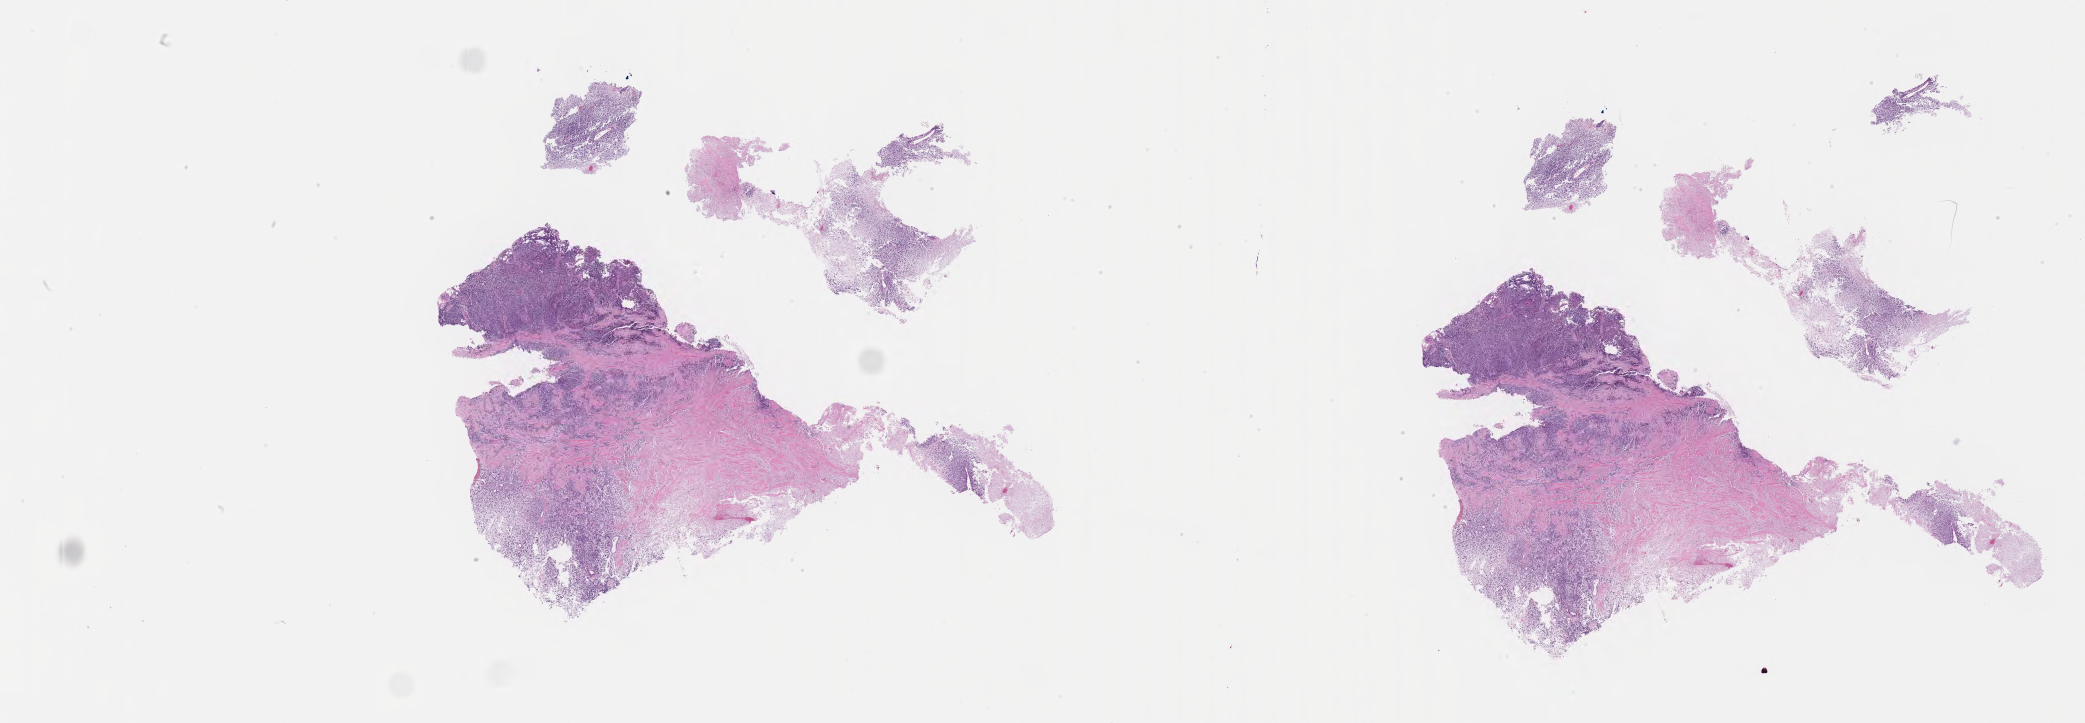
Whole-slide image, H&E stain of tumor tissue from the soft tissue of lower extremity, a low-resolution overview of the entire scanned area, about 33.7 x 11.7 mm, formalin-fixed paraffin-embedded section. Patient: male, age 145 months (12 years 1 month).
Diagnosis (ICD-O-3 morphology term): Sarcoma, NOS.